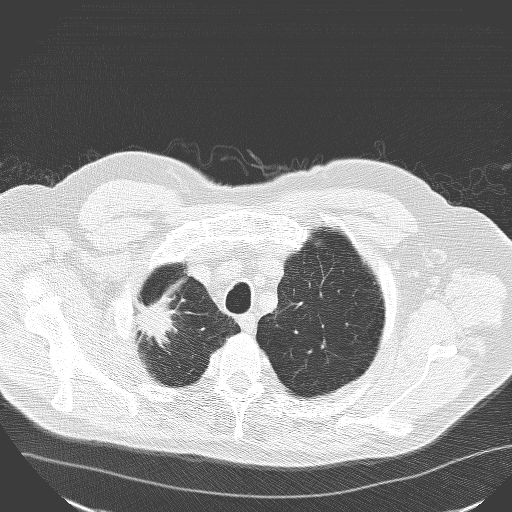
Low-dose screening chest CT, one axial slice. Position 141 of 160 along the scan axis. 120 kVp. Lung window (W 1500 / L -600 HU). 3.2 mm slice thickness. 512 × 512 image matrix.
Structures marked on this image (expert manual segmentation):
- lesion 1 (tumor, upper lobe of right lung): box from (x=136, y=301) to (x=173, y=339) px